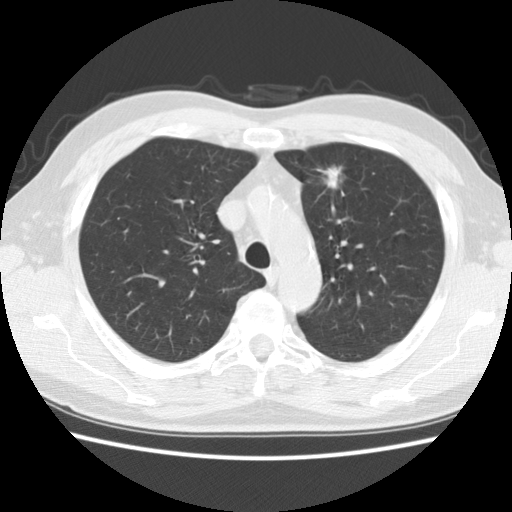
Axial slice from a low-dose chest CT screening exam; second screening round (one year after baseline); lung window (W 1500 / L -600 HU); 2.5 mm slice thickness; standard (soft-tissue) reconstruction kernel (STANDARD); slice 47 of 172 in the series; 512 × 512 image matrix. Male, age 63 years at enrolment. Former smoker at enrolment.
Expert-annotated lung lesion, bounding box [x1, y1, x2, y2] px = [299, 148, 357, 202]. The exam's reader record, not a measurement of the box and not confirmed to be the same lesion: non-calcified nodule or mass ≥4 mm, left upper lobe, 23 × 18 mm, spiculated (stellate) margins, soft tissue attenuation, pre-existing on the prior screen: yes; interval growth: yes. Lung cancer was diagnosed 83 days after this screen: adenocarcinoma, NOS, left upper lobe, moderately differentiated (G2), stage IA (AJCC 6th edition), 14 mm at pathology.